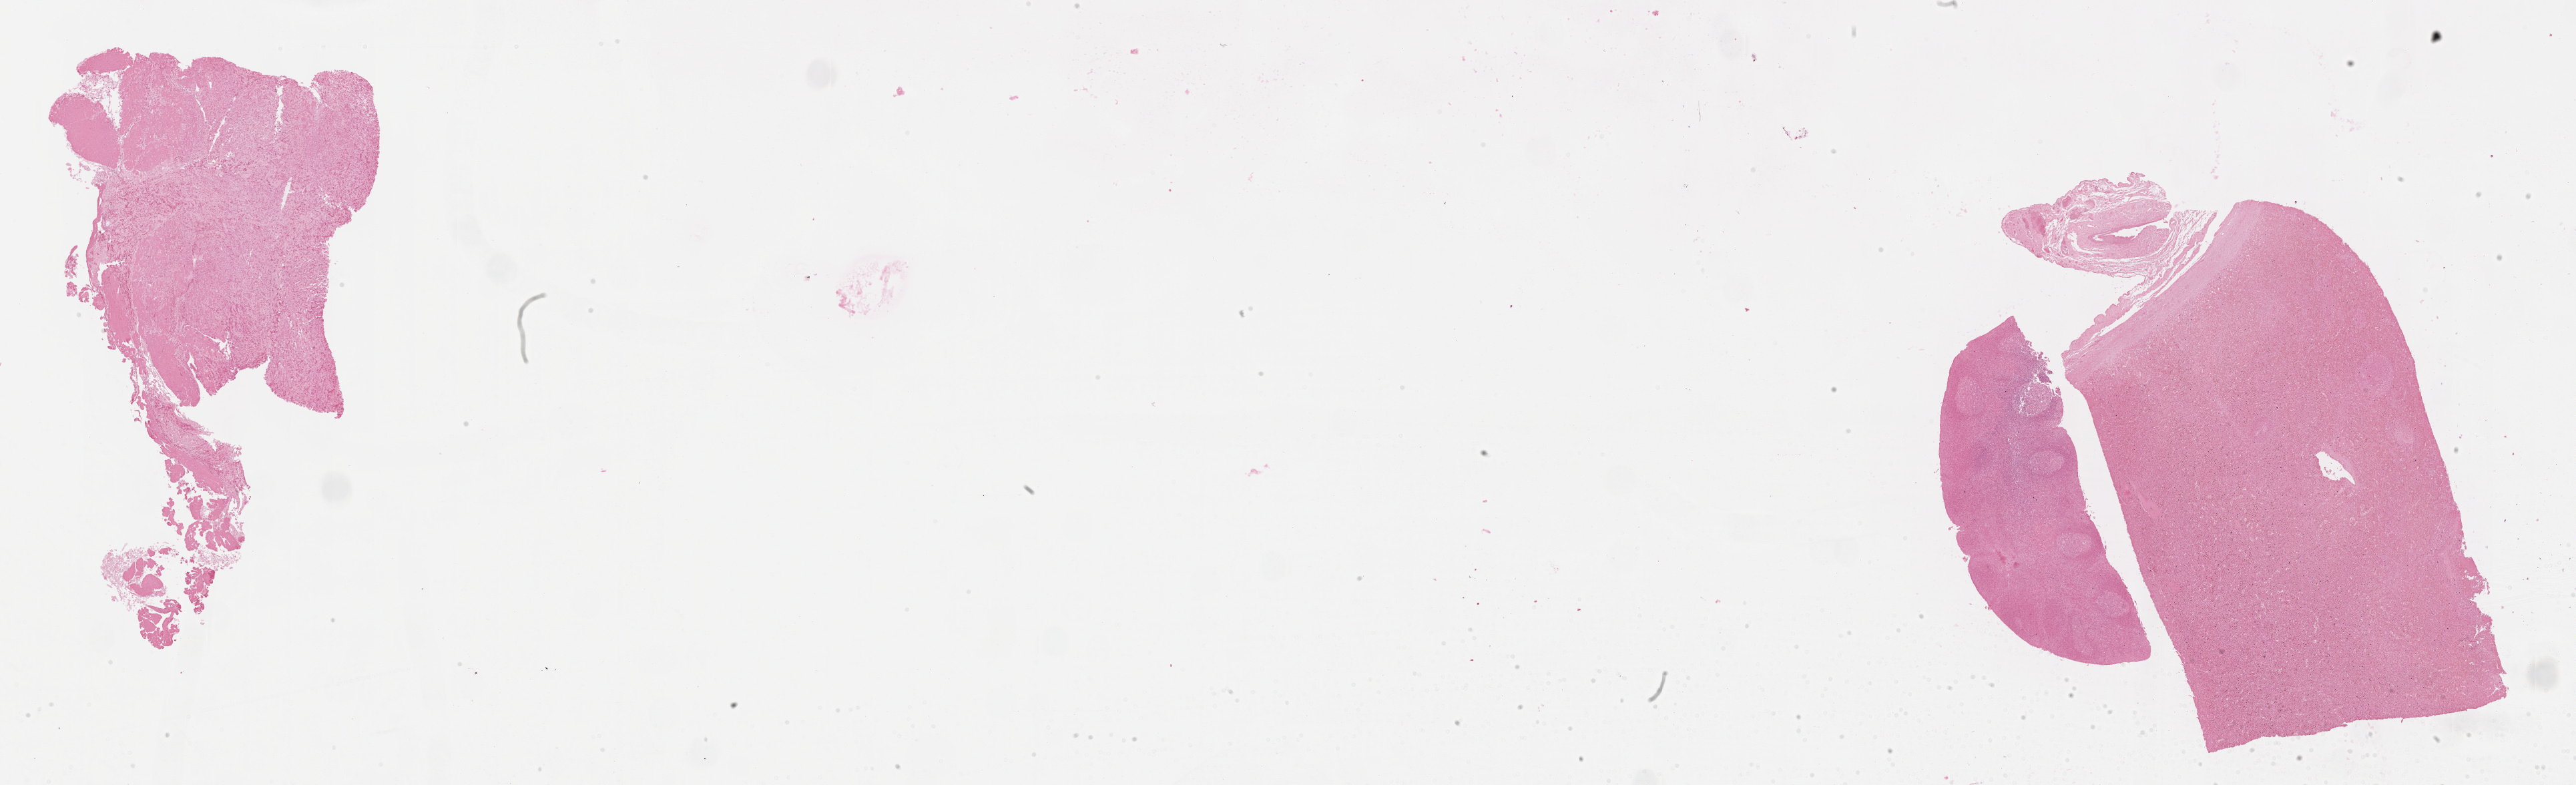
In-situ hybridisation whole-slide image, Epstein–Barr virus-encoded RNA (EBER) probe, low-resolution overview of the scanned area, about 31.2 x 9.5 mm. Tumor tissue. Site: kidney. Patient: male, age 12 years.
Diagnosis: Diffuse large B-cell lymphoma, NOS.